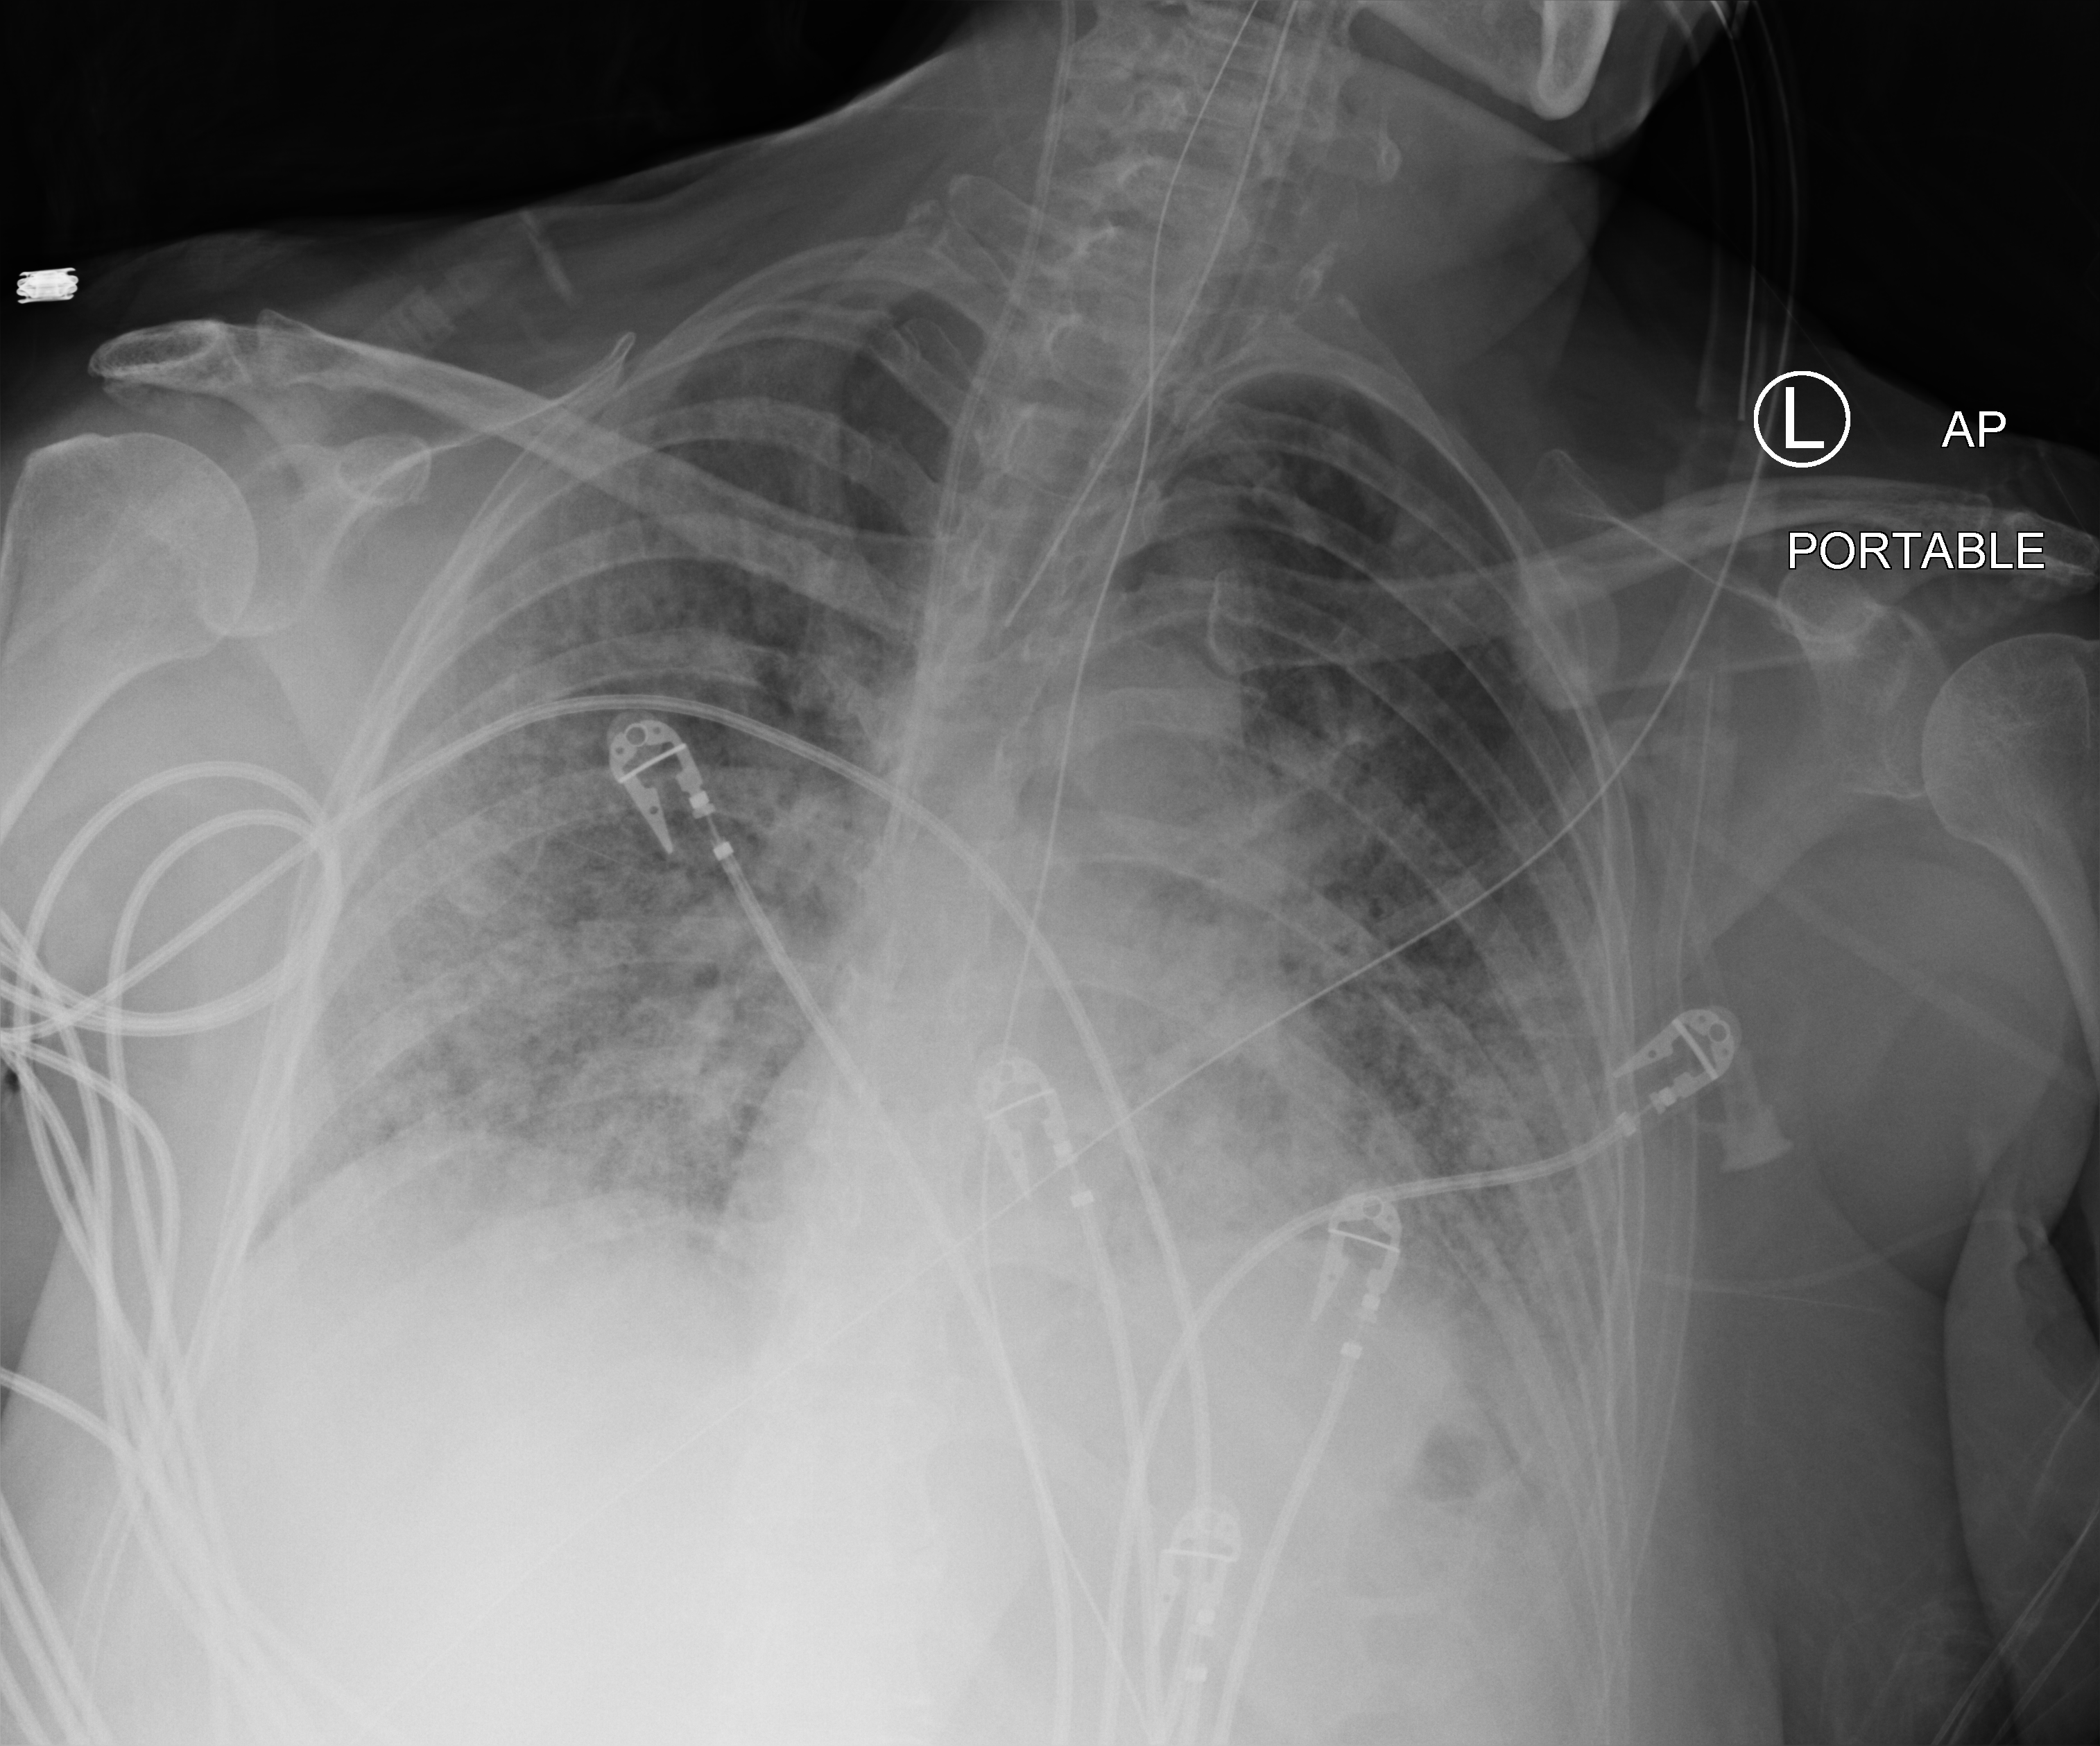
Bedside chest radiograph (computed radiography), anteroposterior (AP) projection. Female patient hospitalised with COVID-19, age 60–74 years.
Admission-level facts for this patient (not findings on this image; timing relative to this image not recorded): mechanically ventilated during this hospital stay: yes; admitted to intensive care during this hospital stay: yes.